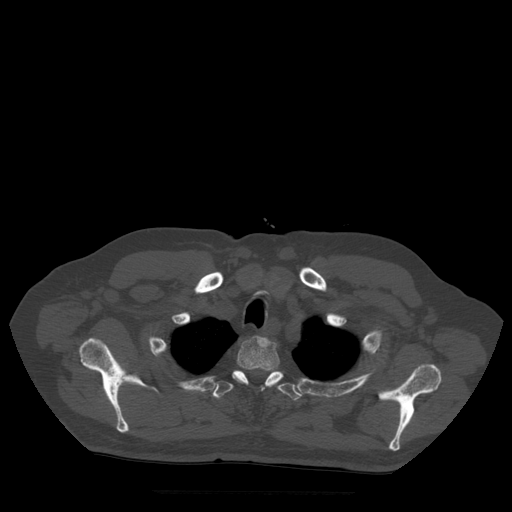
CT including the spine, one axial slice; position 418 of 522 along the scan axis; bone window (W 1800 / L 400 HU); 1.25 mm slice thickness; 512 × 512 image matrix, field of view 420 × 420 mm. Patient age 72 years. From the clinical record (not read from this slice): primary cancer: prostate.
Annotated regions visible in this slice (semi-automatic segmentation, software-assisted and operator-edited):
- T2 vertebra: bounding box (x1, y1, x2, y2) in pixels: (233, 336, 284, 391)
- T3 vertebra: (212, 371, 304, 401)